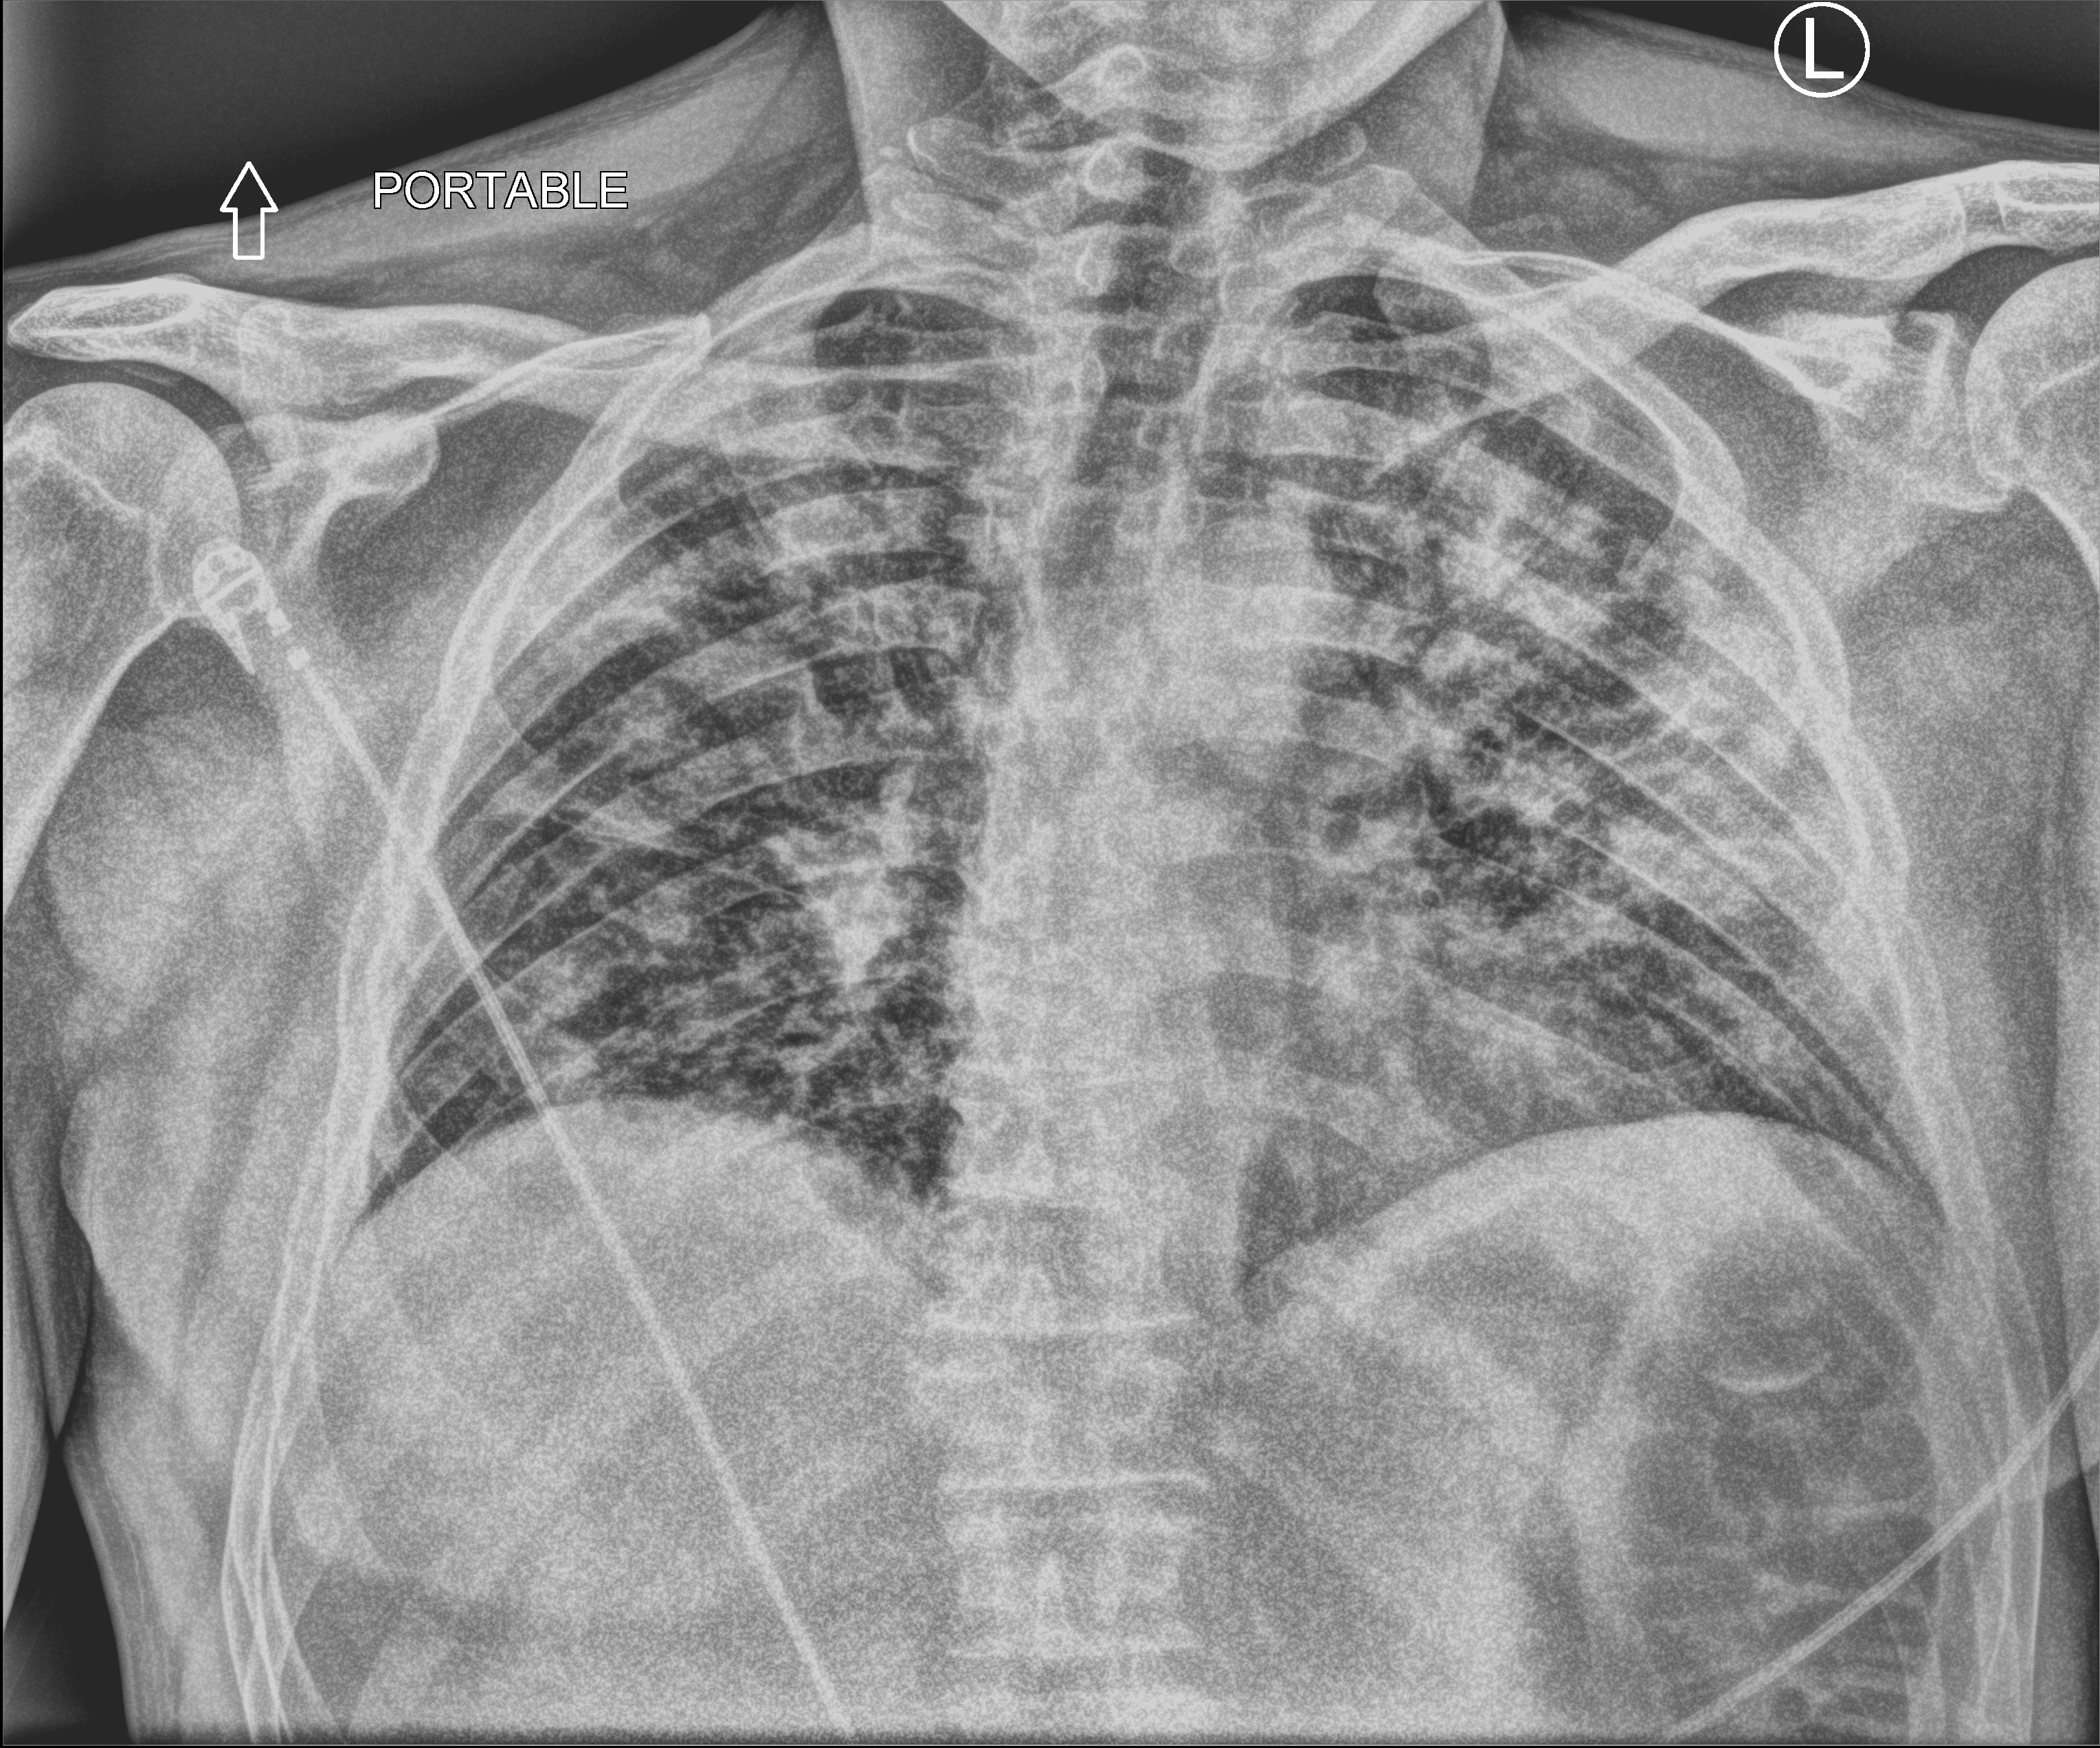
Bedside chest radiograph (computed radiography), anteroposterior (AP) projection. Male patient hospitalised with COVID-19, age 18–59 years.
From the hospital-stay record, not from the radiograph (when in the stay this image was taken is not recorded): mechanically ventilated during this hospital stay: no.